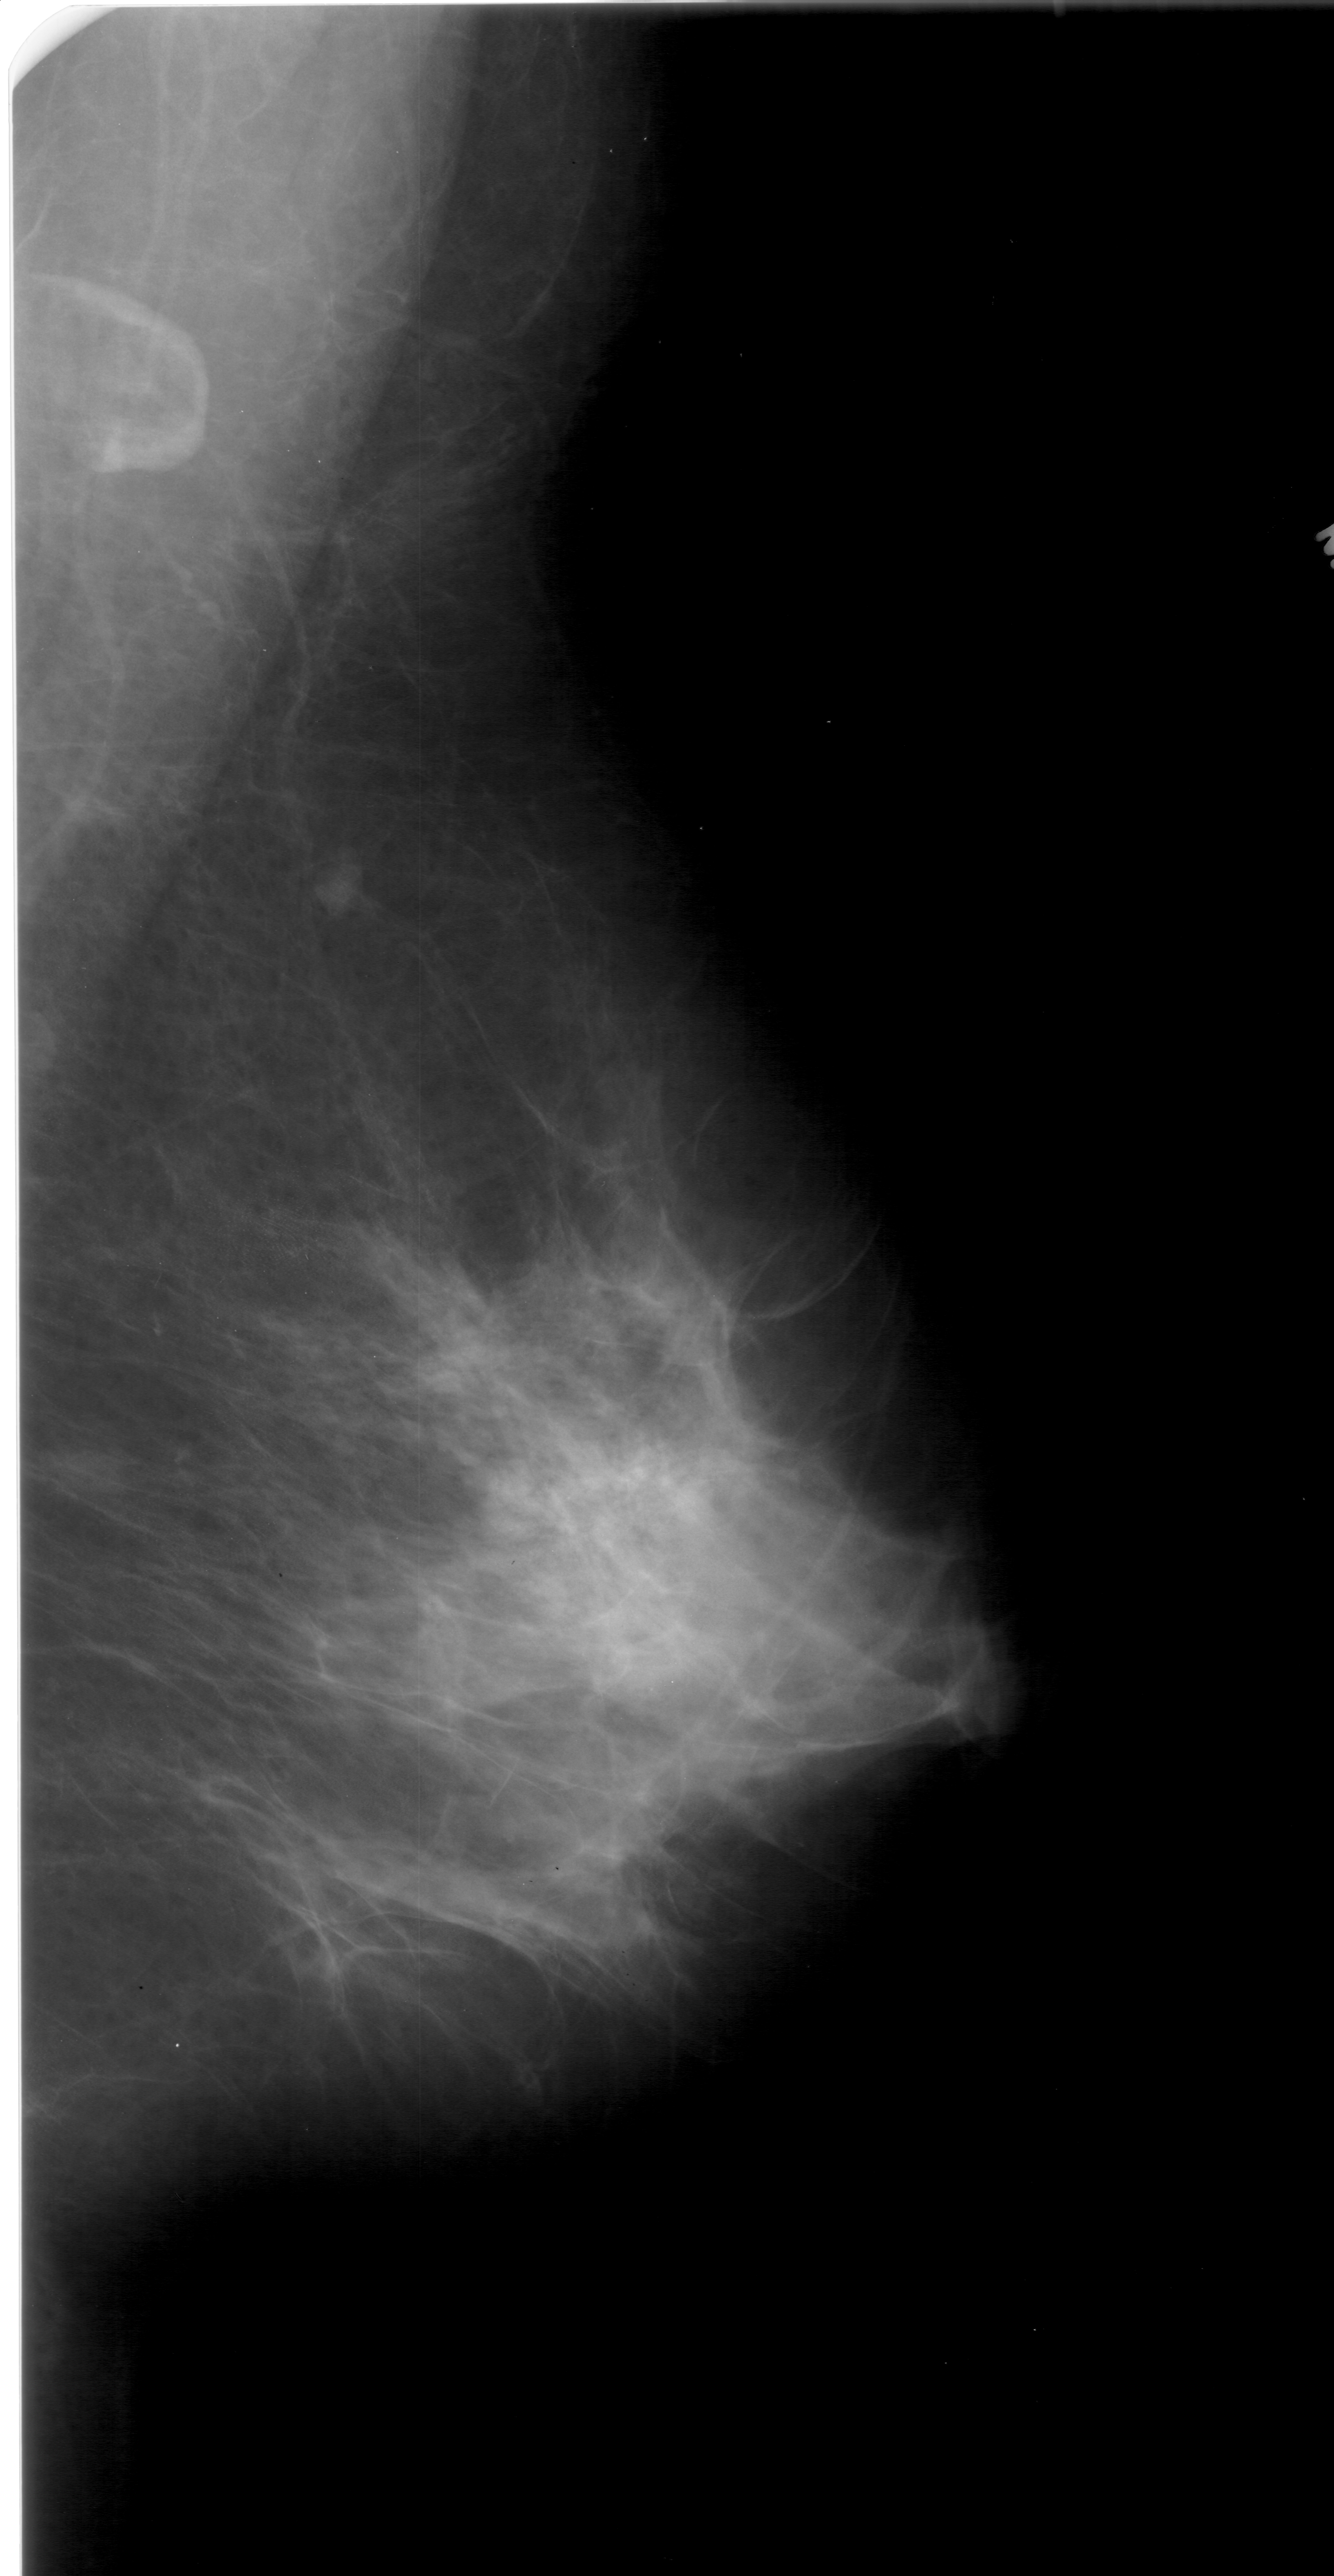
Scanned film-screen mammogram, right breast, MLO view, BI-RADS breast density category 4 (scale 1–4).
Radiologist-marked abnormalities on this image: mass, shape architectural distortion, margins spiculated; BI-RADS assessment category 4; subtlety rating 4 on a 1 (subtle) to 5 (obvious) scale; pathology result (as recorded, not read from the image): benign.